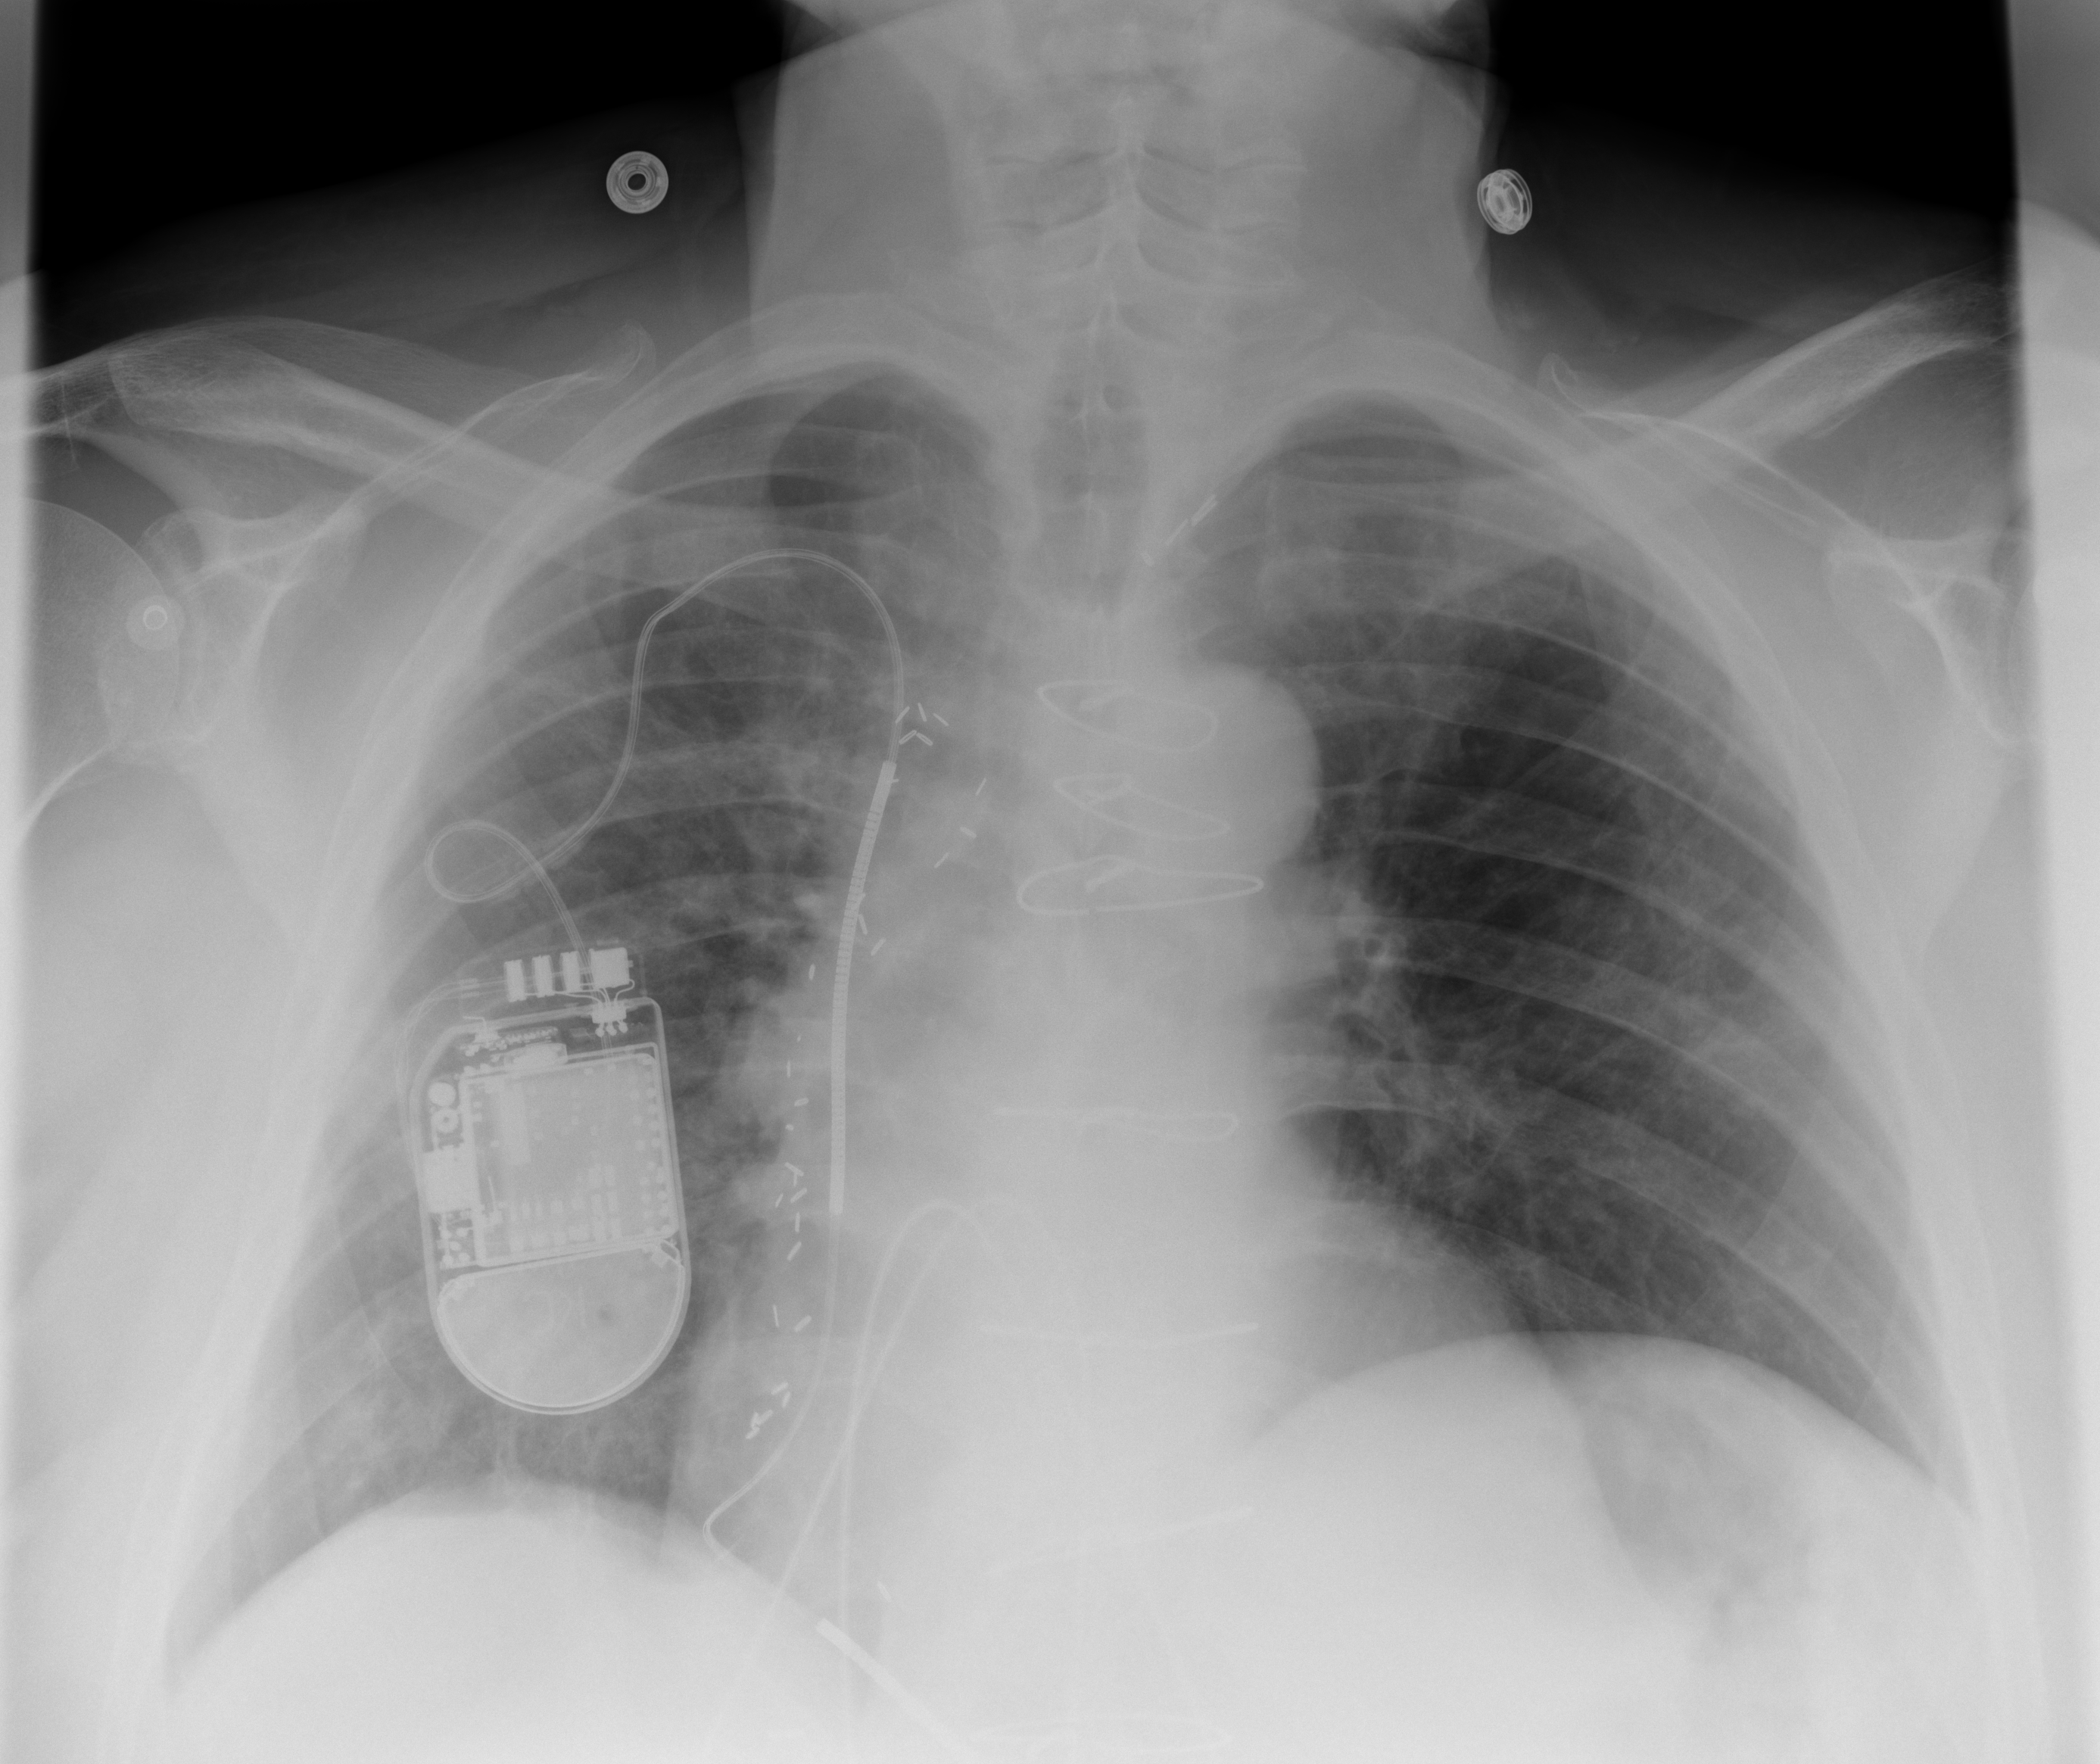
Chest X-ray (portable), AP projection. Male patient, age 70 years; imaged 28 days after the COVID-19 diagnosis.
Radiologist's key findings for this exam: Subtle patchy airspace disease in the right lung base.